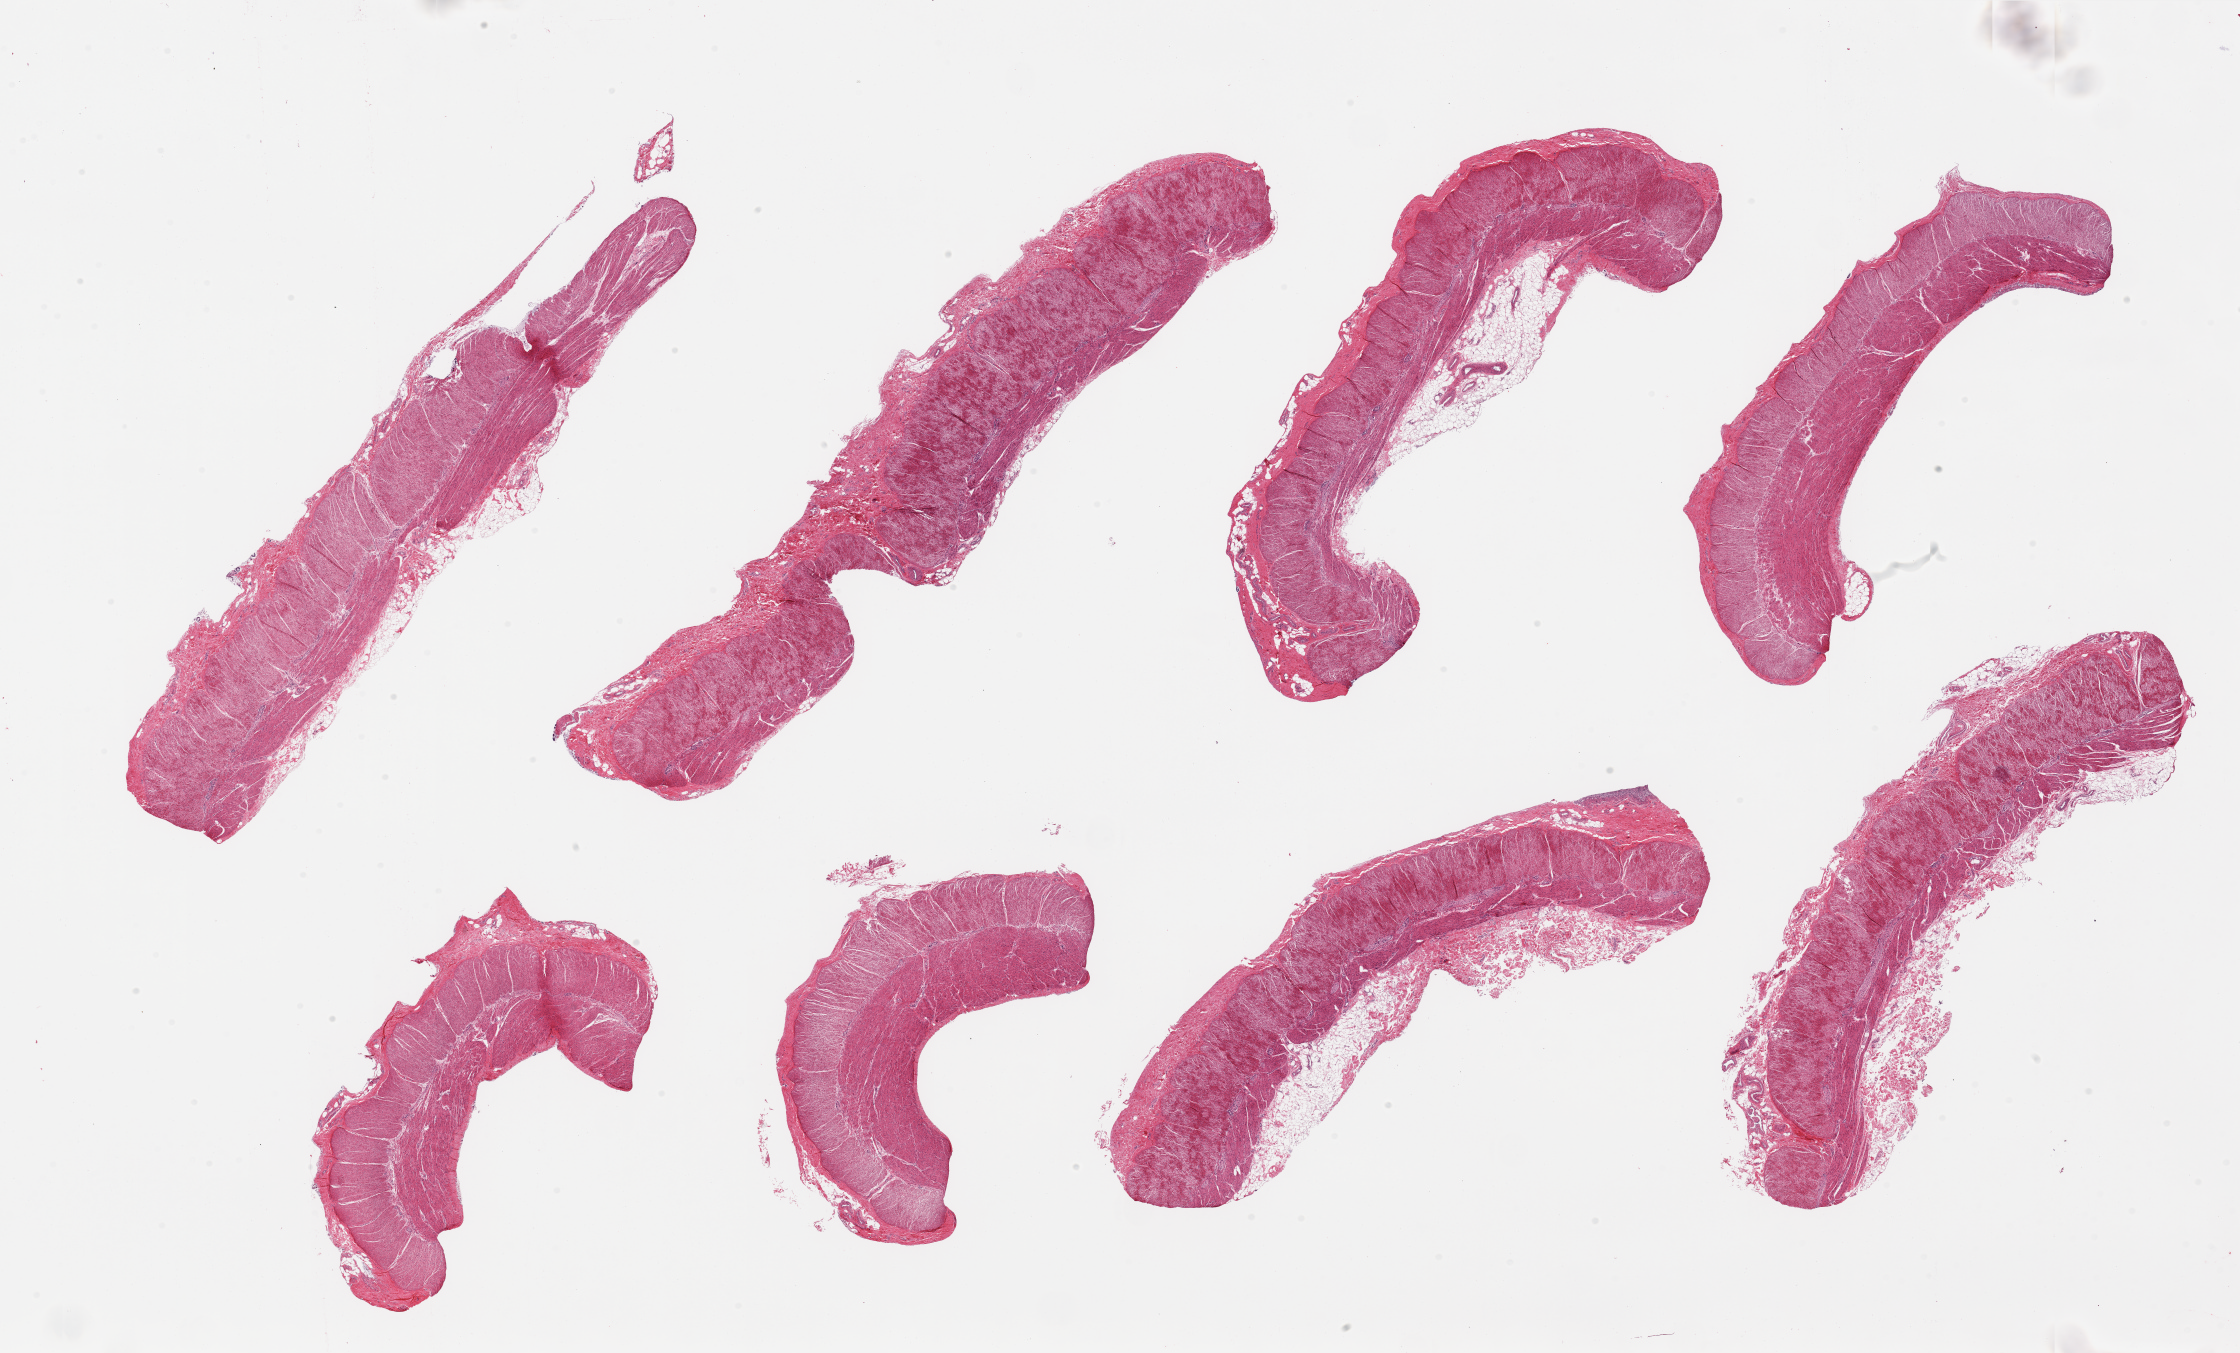
Digitized hematoxylin and eosin (H&E)-stained section, a low-resolution overview of the entire scanned area, about 35.4 x 21.4 mm (slide scanned at 20x); PAXgene-fixed paraffin-embedded (PFPE) section; target tissue: sigmoid colon; tissue donor sample. Male donor.
- review note (as recorded): 8 pieces; some include residual attached fat/submucosa